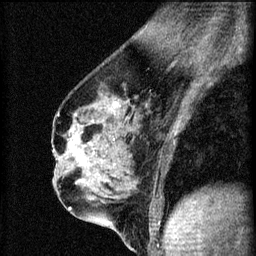
Breast MRI (dynamic contrast-enhanced), one sagittal slice. Slice 36 of 60 in the series (ordered by position). 3 images stored at this slice position (order not interpretable as contrast timing). 1.5 T. TE 4.2 ms, TR 8.2 ms. 256 × 256 image matrix. Patient: female, 56 years.
Outlined on this slice (semi-automatically segmented with operator editing):
- analysis volume of interest (the breast-tissue region the enhancement analysis was run in; not a lesion): box from (x=62, y=136) to (x=111, y=179) px
- tumour enhancement mask (voxels above the 70 % enhancement threshold inside the analysis volume of interest): (x=70, y=136)–(x=78, y=149)